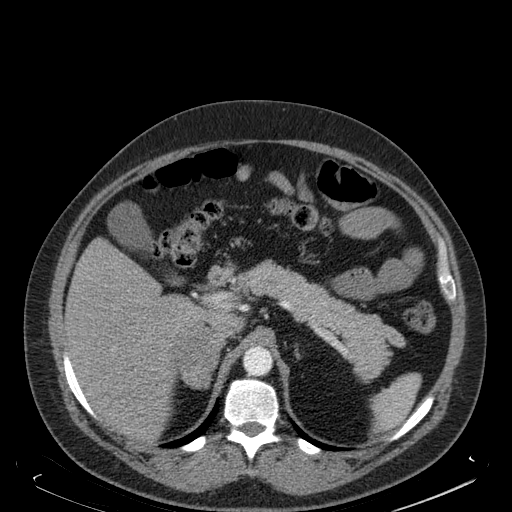
Contrast-enhanced abdominal CT, one axial slice. Slice 122 of 181 in the series (ordered by position). Soft-tissue window (W 400 / L 40 HU). 1.5 mm slice thickness. 512 × 512 image matrix, field of view 405 × 405 mm. Male patient. From the clinical record (not read from this slice): diagnosis: adrenocortical carcinoma; tumour side: right adrenal; tumour size at pathology: 7.5 cm; Ki-67 index: 25 %; stage (as recorded): 4.
Outlined on this slice (semi-automatically segmented with operator editing):
- mass: bounding box <177,323,219,389> (left, top, right, bottom; pixels)